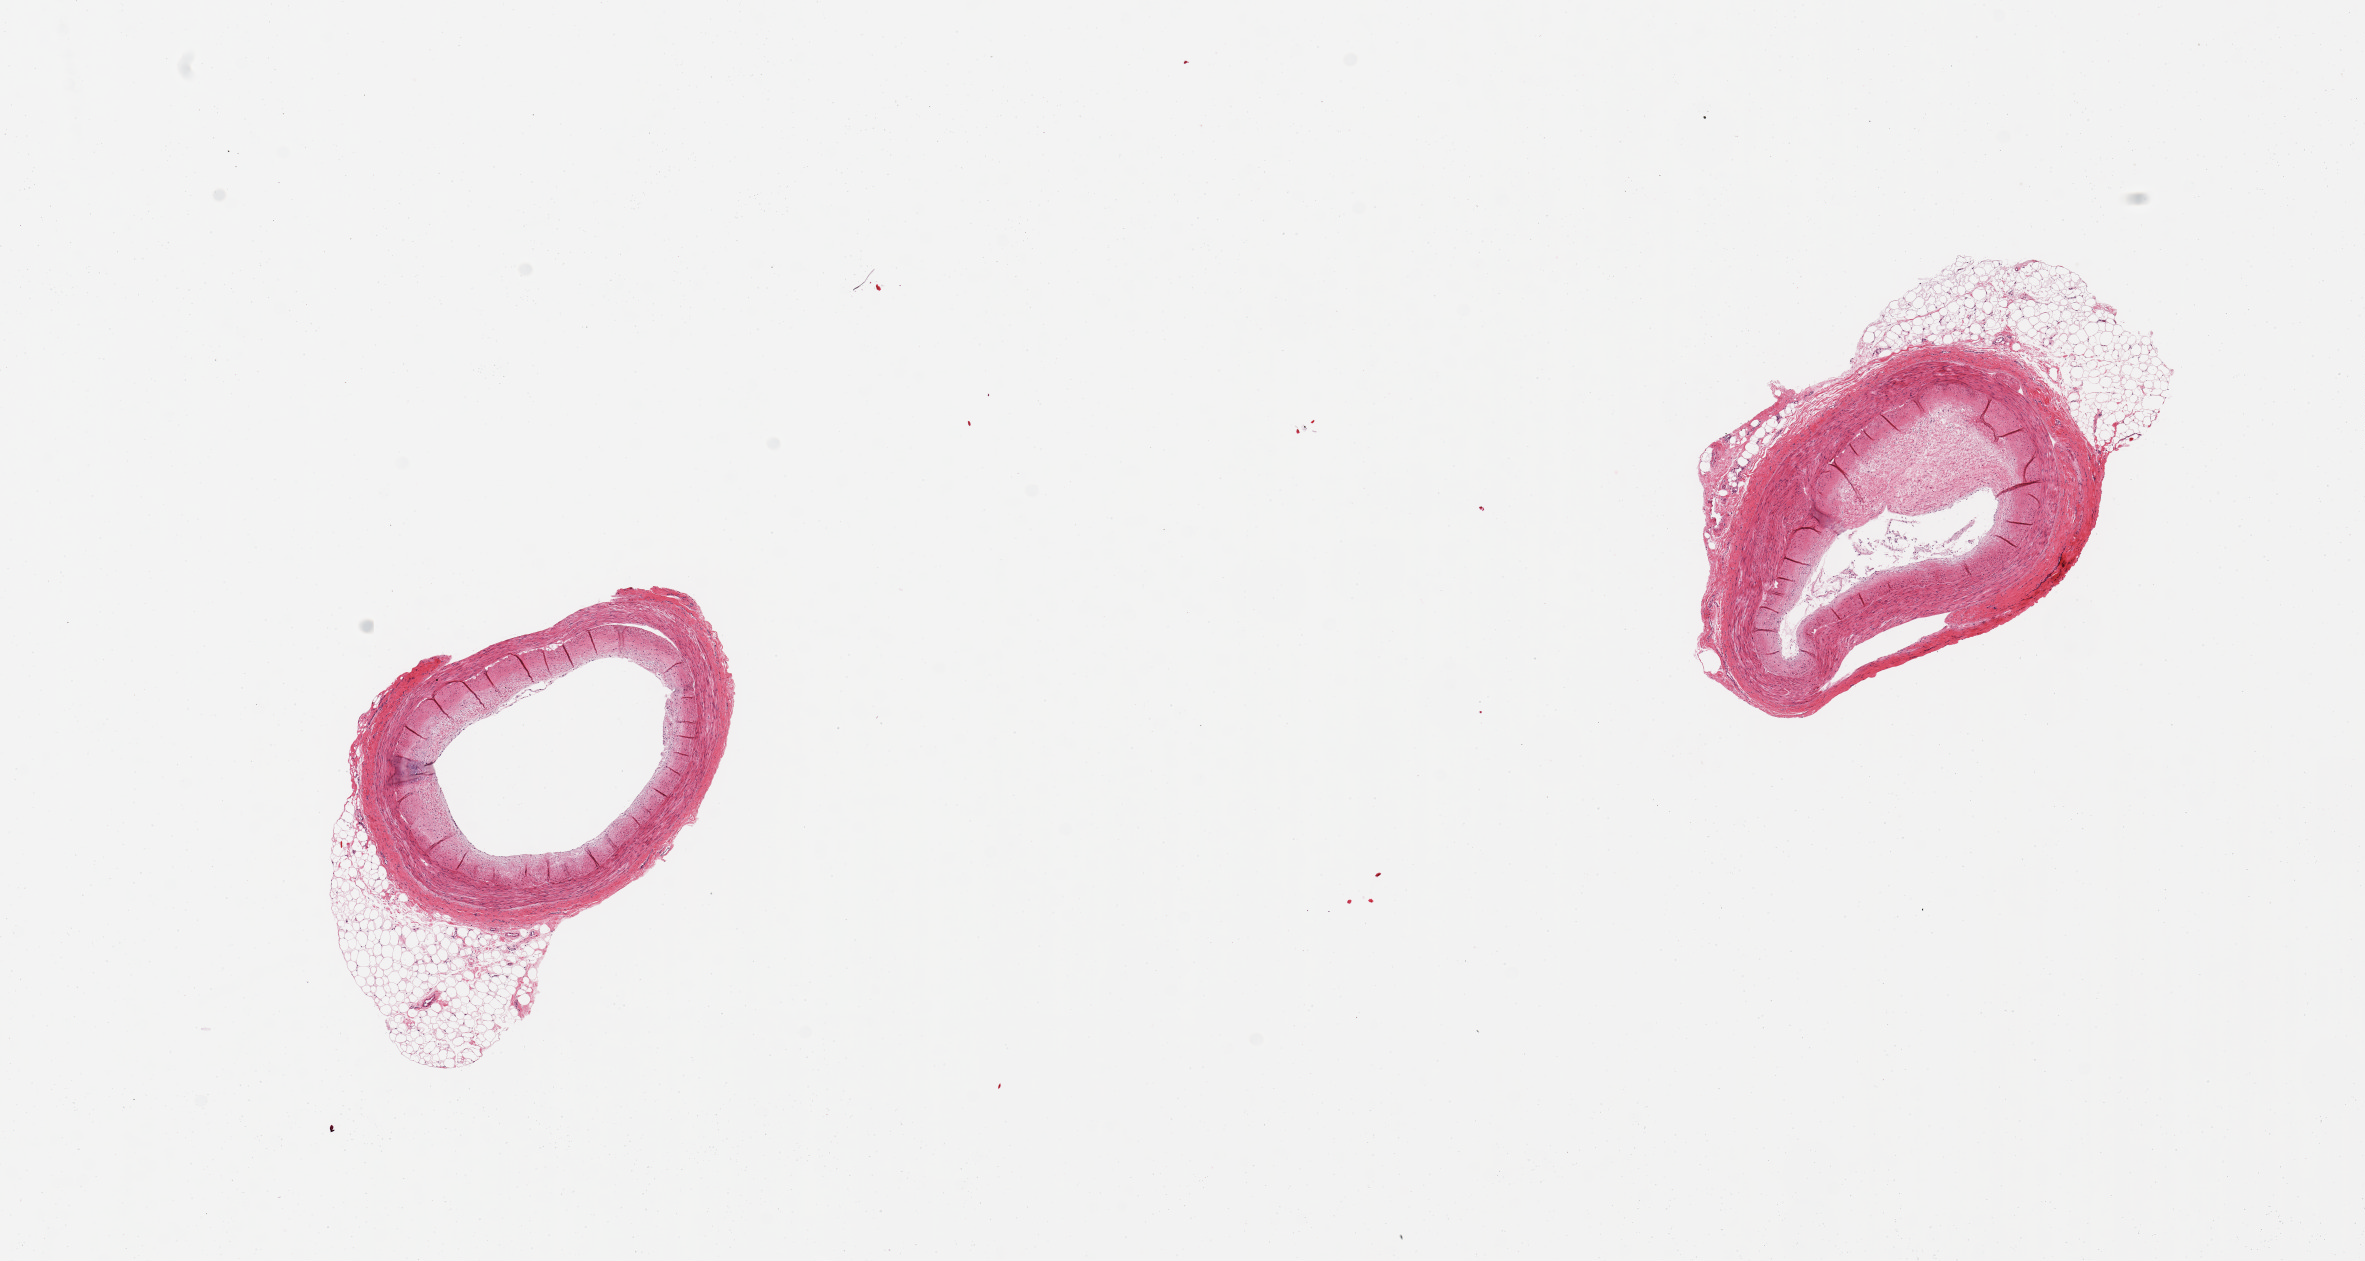
Whole-slide image, H&E stain — a low-resolution overview of the entire scanned area, about 18.7 x 10.0 mm. PAXgene-fixed, paraffin-embedded tissue. Target tissue: coronary artery. Tissue donor sample.
- reviewer comment on this tissue sample: 2 pieces, nubbin of adherent fat, ~1mm